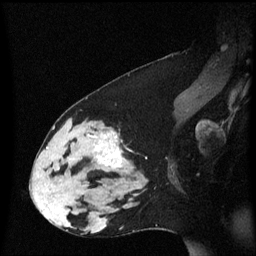
Breast MRI (dynamic contrast-enhanced), one sagittal slice; slice 35 of 60 in the series (ordered by position); dynamic contrast-enhanced series, image 2 of 3 at this slice position (ordered by acquisition); 1.5 T; TE 4.2 ms, TR 8.4 ms; 2 mm slice thickness; 256 × 256 image matrix, field of view 210 × 210 mm. Patient: female, 33 years. From the clinical record (not read from this slice): setting: breast cancer imaged before/during neoadjuvant chemotherapy; receptor status: triple-negative.
Annotated regions visible in this slice (semi-automatically segmented with operator editing):
- analysis volume of interest (the breast-tissue region the enhancement analysis was run in; not a lesion): bounding box <44,123,139,189> (left, top, right, bottom; pixels)
- tumour enhancement mask (voxels above the 70 % enhancement threshold inside the analysis volume of interest): <57,132,124,171>